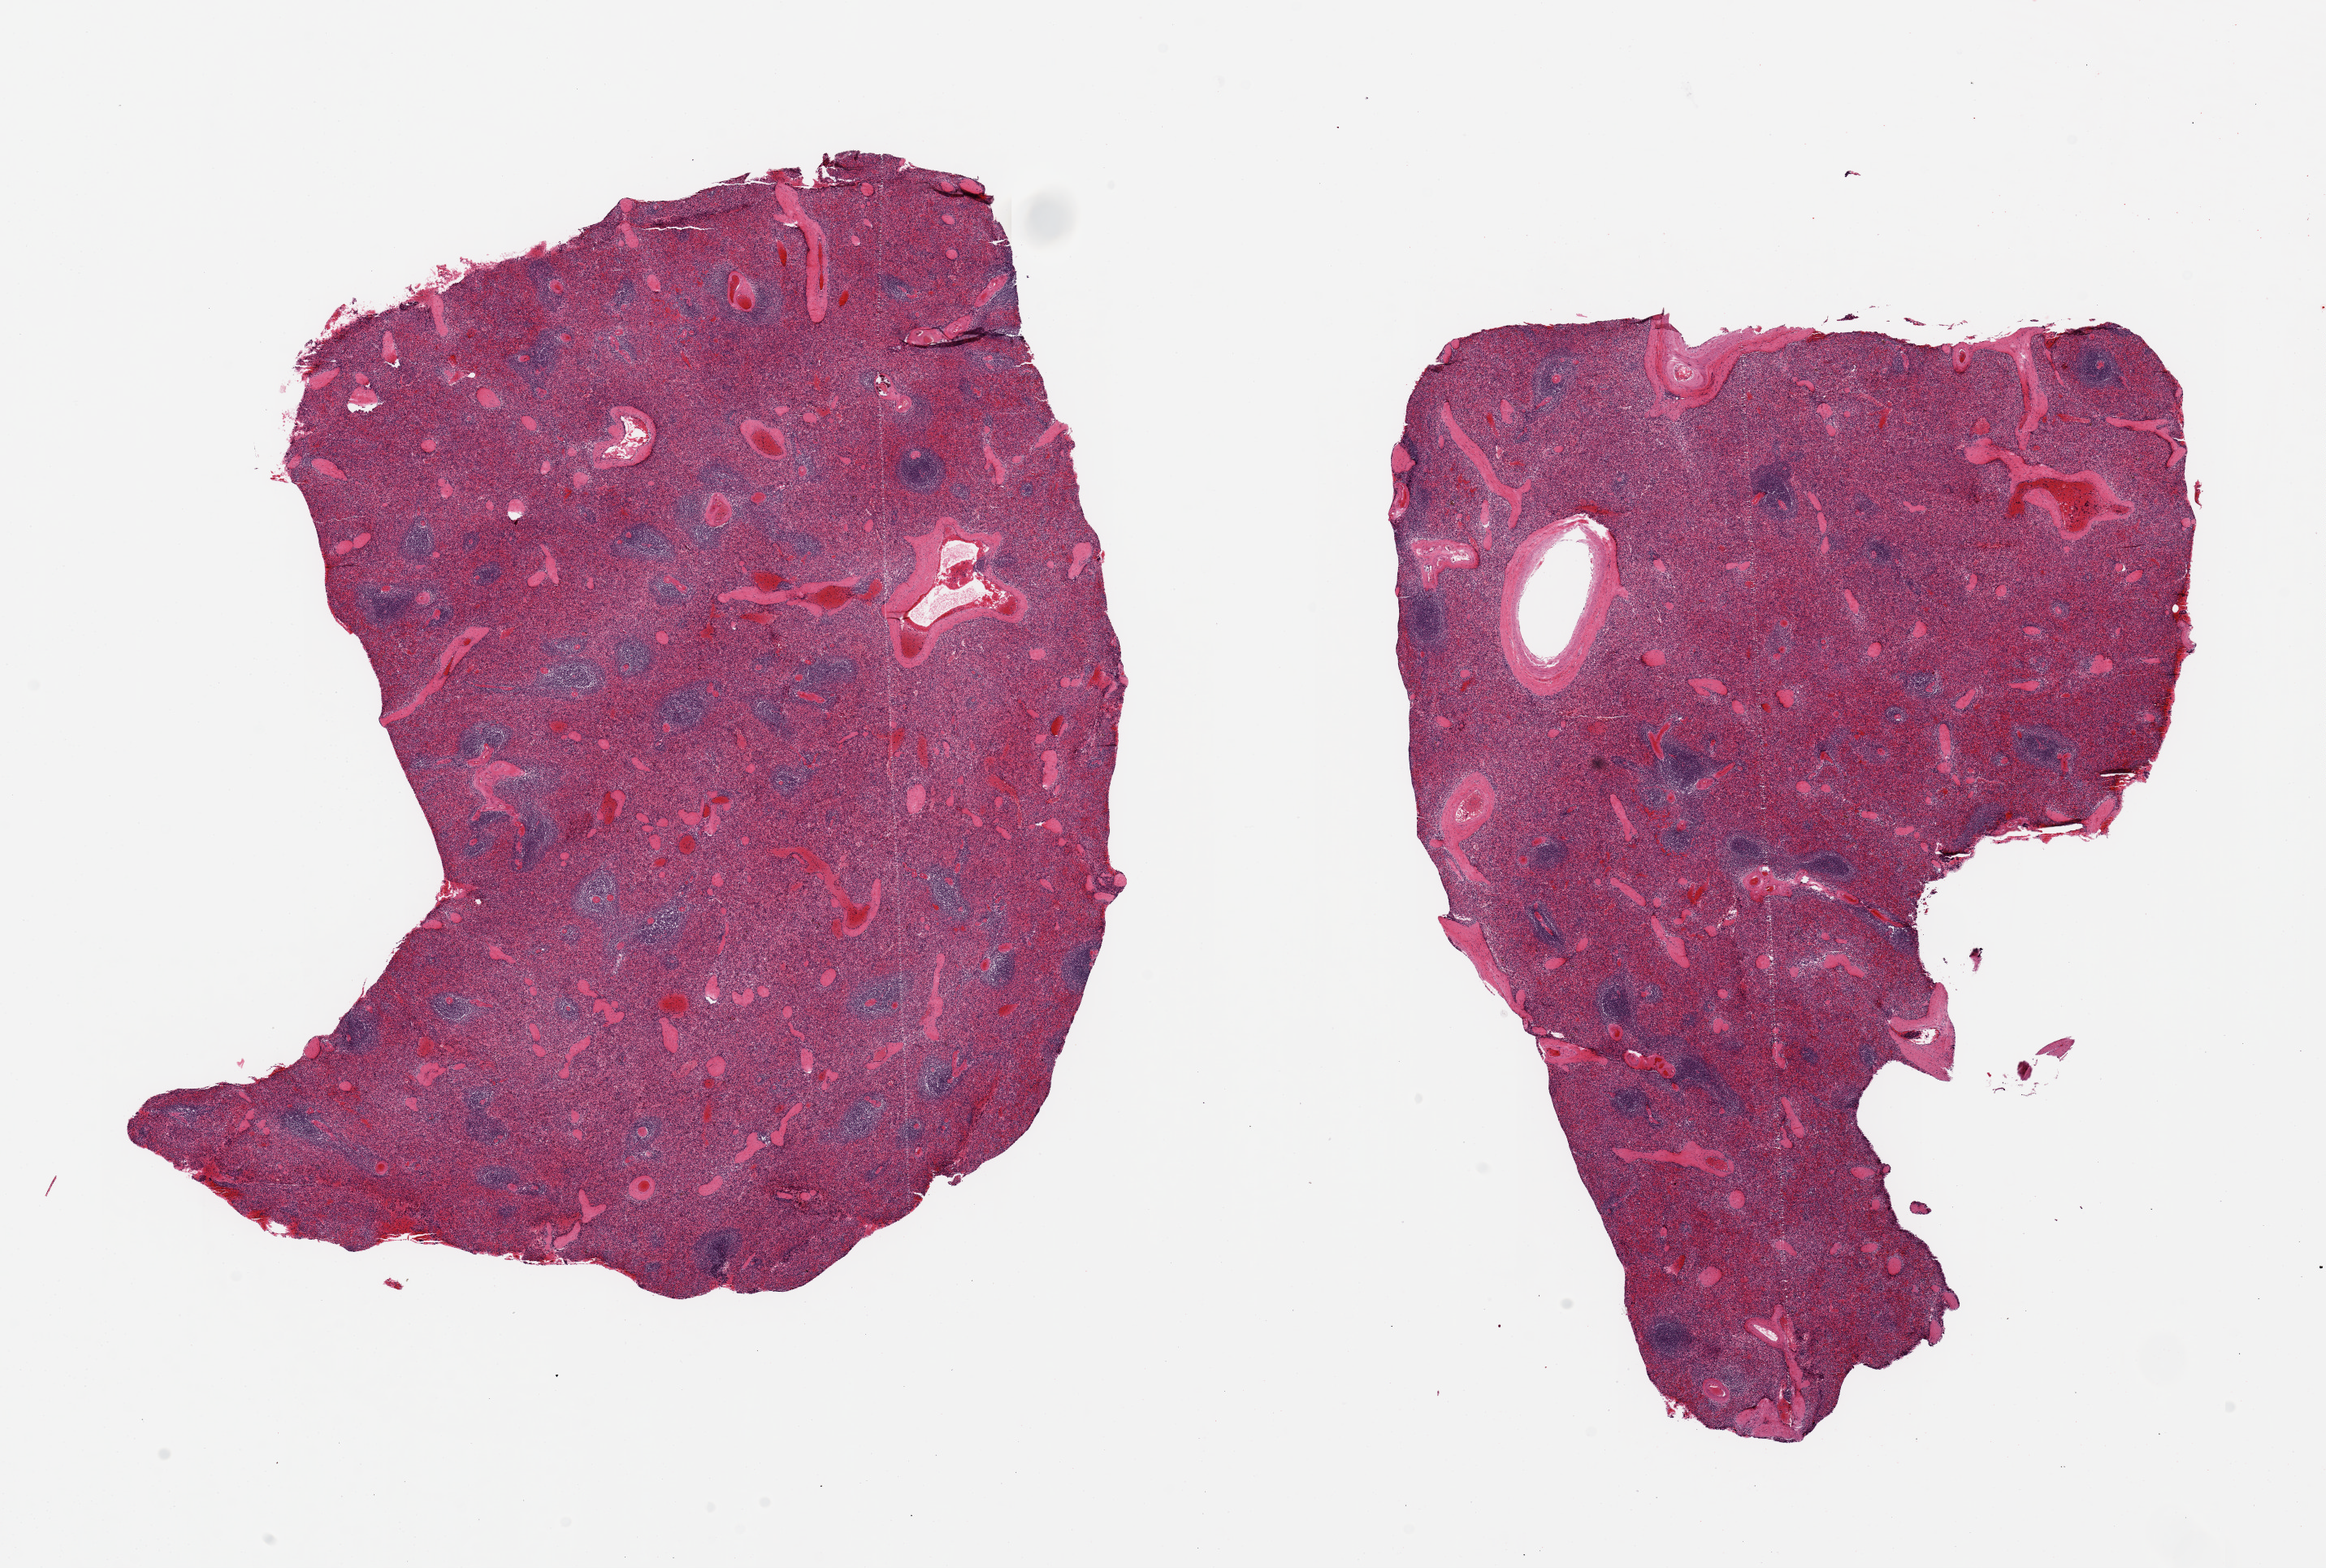
Hematoxylin and eosin (H&E) whole-slide image — shown as a low-resolution overview of the whole scanned area (about 22.6 x 15.3 mm, acquisition: 20x scan), PAXgene-fixed, paraffin-embedded tissue, target tissue: spleen, donor tissue sample. Female donor.
Pathologist's review note for this sample: 2 pieces, 11x8 & 11x7mm. Slight congestion and good lymphoid tissue.